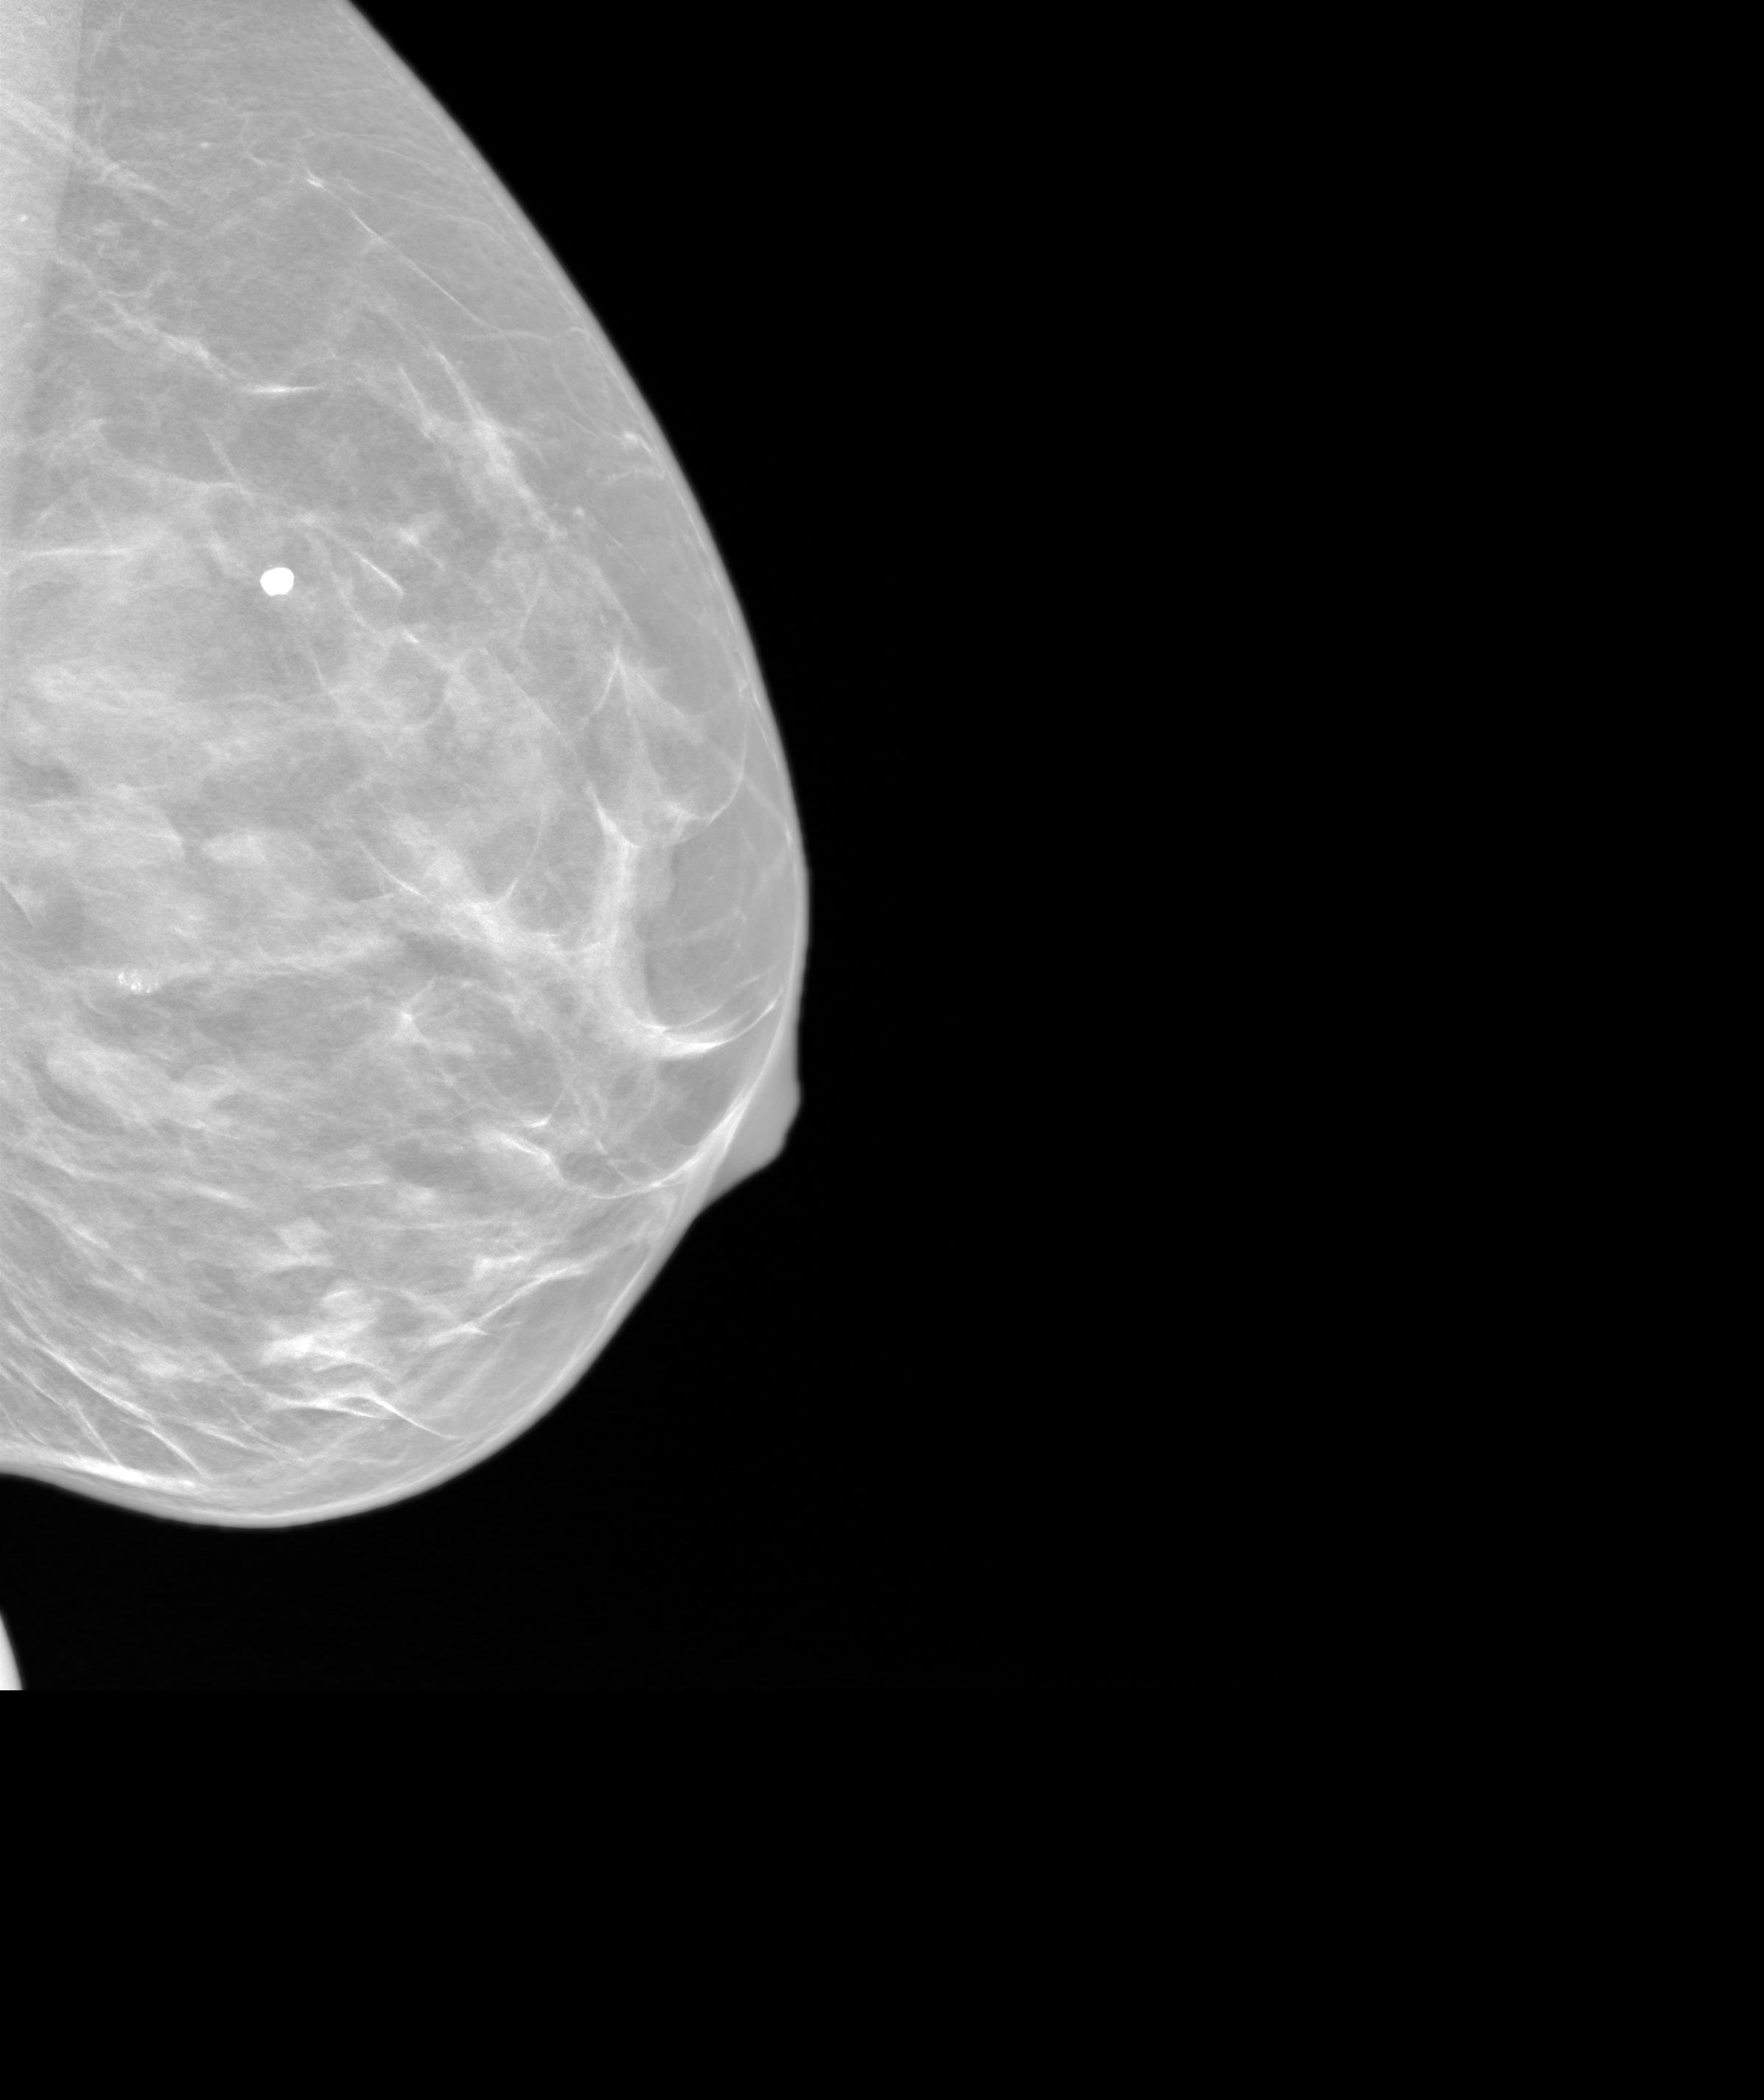
Diagnostic examination (additional views). Patient: female, 52 years.
Image type: synthesized 2-D view from tomosynthesis. Breast: left. Projection: lateromedial (LM) view.